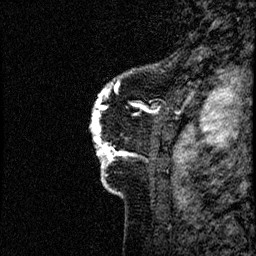
Breast MRI (dynamic contrast-enhanced), one sagittal slice. Slice 8 of 60 in the series (ordered by position). Dynamic contrast-enhanced study with each time point stored as its own series, time point 2 of 4 at this slice position (early post-contrast, ordered by acquisition time). 1.5 T. TE 4.2 ms, TR 17.6 ms. 2 mm slice thickness. 256 × 256 image matrix. Female patient, age 40 years. Case-level facts recorded for this patient, not image findings: setting: breast cancer imaged before/during neoadjuvant chemotherapy; receptor status: HER2-positive.
Outlined on this slice (semi-automatic segmentation, software-assisted and operator-edited):
- analysis volume of interest (the breast-tissue region the enhancement analysis was run in; not a lesion): bounding box (x1, y1, x2, y2) in pixels: (88, 56, 185, 206)
- tumour enhancement mask (voxels above the 100 % enhancement threshold inside the analysis volume of interest): (90, 87, 159, 171)